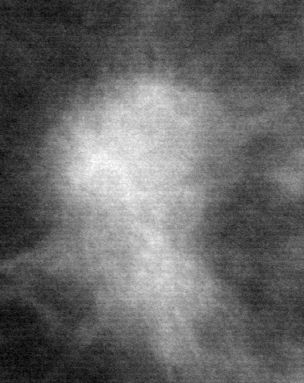
Crop from a digitized film mammogram around one marked abnormality; left breast; MLO view.
Finding: mass, shape lobulated, margins spiculated; BI-RADS assessment category 5; pathology (as recorded): malignant.